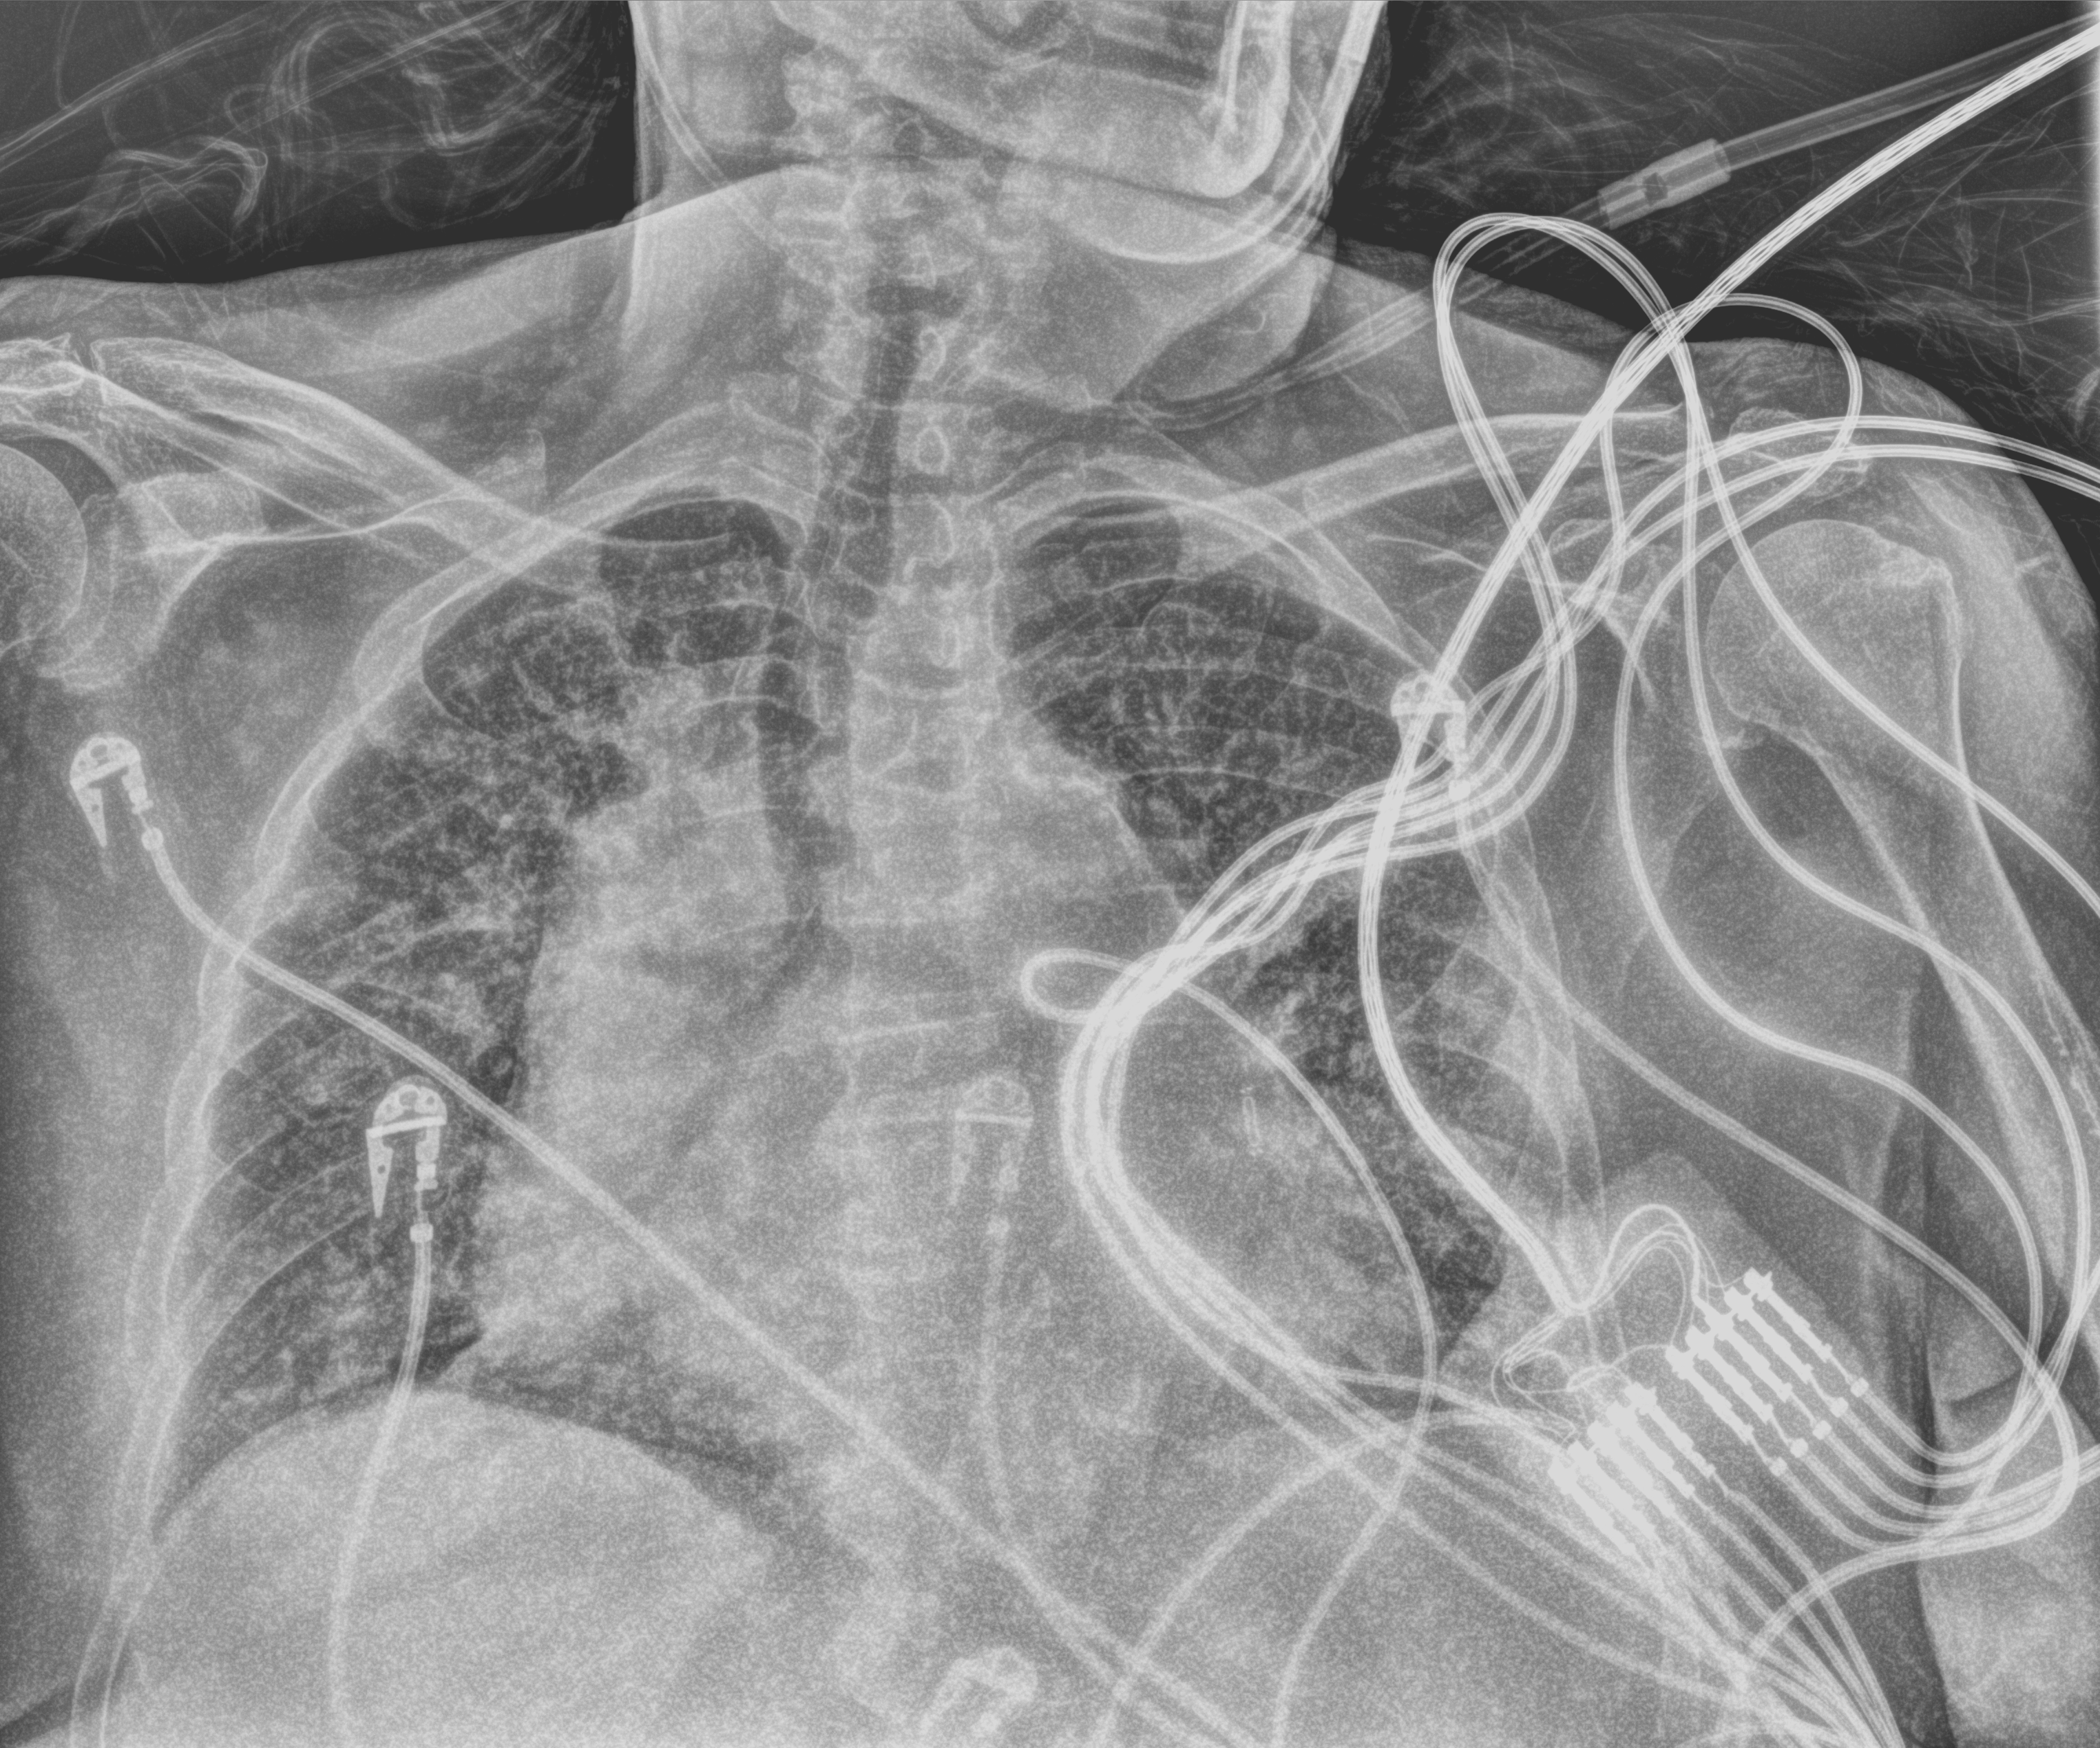
Chest X-ray (portable); anteroposterior (AP) projection. Female patient hospitalised with COVID-19, age 75–90 years.
Hospital-stay facts (about this admission, not read from this image; timing relative to this image not recorded):
- length of hospital stay: 10 days